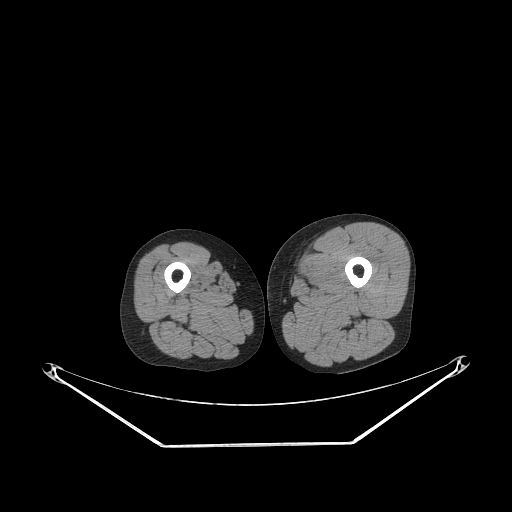
CT of an extremity soft-tissue mass (from a PET/CT study), one axial slice. 140 kVp. Soft-tissue window (W 400 / L 40 HU). 3.75 mm slice thickness. 512 × 512 image matrix, field of view 500 × 500 mm. Male patient. Case-level facts recorded for this patient, not image findings: histological type: pleiomorphic leiomyosarcoma; grade: high; site of the primary tumour: left thigh.
Annotated regions visible in this slice (expert contour drawn on MRI and transferred to this co-registered scan by the dataset authors):
- gross tumour volume including surrounding oedema: bounding box [x1, y1, x2, y2] px = [290, 260, 312, 286]